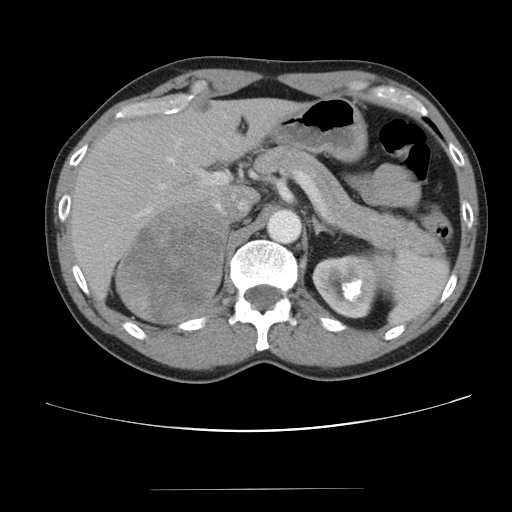
Contrast-enhanced abdominal CT, one axial slice. Position 65 of 80 along the scan axis. Reconstruction kernel STANDARD. Soft-tissue window (W 400 / L 40 HU). 5 mm slice thickness. 512 × 512 image matrix. Patient: male, 61 years. From the clinical record (not read from this slice): diagnosis: adrenocortical carcinoma; tumour side: right adrenal; tumour size at pathology: 11.1 cm; Ki-67 index: 32 %; stage (as recorded): 2.
Annotated regions visible in this slice (semi-automatic segmentation, software-assisted and operator-edited):
- mass: bounding box <118,206,225,322> (left, top, right, bottom; pixels)